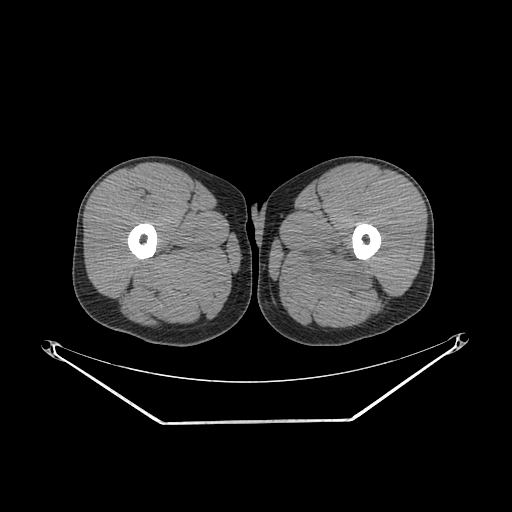
CT of an extremity soft-tissue mass (from a PET/CT study), one axial slice; slice 244 of 267 in the series (ordered by position); 140 kVp; soft-tissue window (W 400 / L 40 HU); 3.75 mm slice thickness; 512 × 512 image matrix, field of view 500 × 500 mm. Male patient. Case-level facts recorded for this patient, not image findings: histological type: extraskeletal osteosarcoma; grade: high; site of the primary tumour: left adductur.
Structures marked on this image (expert contour drawn on MRI and transferred to this co-registered scan by the dataset authors):
- gross tumour volume (mass): bounding box [x1, y1, x2, y2] px = [288, 240, 378, 298]